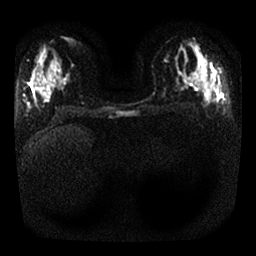
Breast MRI, one axial slice; slice 15 of 25 in the series (ordered by position); diffusion-weighted series; image 2 of 4 stored at this slice position (different b-values; order by instance number); 1.5 T; 4 mm slice thickness; 256 × 256 image matrix, field of view 320 × 320 mm. Female patient.
Annotated regions visible in this slice (outlined manually by an expert reader):
- tumour on diffusion-weighted imaging: bounding box <209,64,214,71> (left, top, right, bottom; pixels)